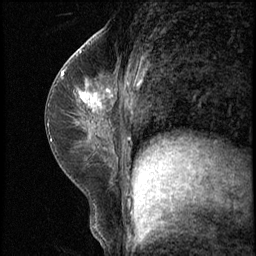
Breast MRI (dynamic contrast-enhanced), one sagittal slice. Slice 31 of 62 in the series (ordered by position). 3 images stored at this slice position (order not interpretable as contrast timing). 1.5 T. TE 4.2 ms, TR 8.7 ms. 256 × 256 image matrix, field of view 180 × 180 mm. Female patient, age 35 years. From the clinical record (not read from this slice): setting: breast cancer imaged before/during neoadjuvant chemotherapy; receptor status: HER2-positive.
Outlined on this slice (semi-automatic segmentation, software-assisted and operator-edited):
- analysis volume of interest (the breast-tissue region the enhancement analysis was run in; not a lesion): bounding box [x1, y1, x2, y2] px = [71, 78, 120, 139]
- tumour enhancement mask (voxels above the 140 % enhancement threshold inside the analysis volume of interest): [81, 93, 100, 105]